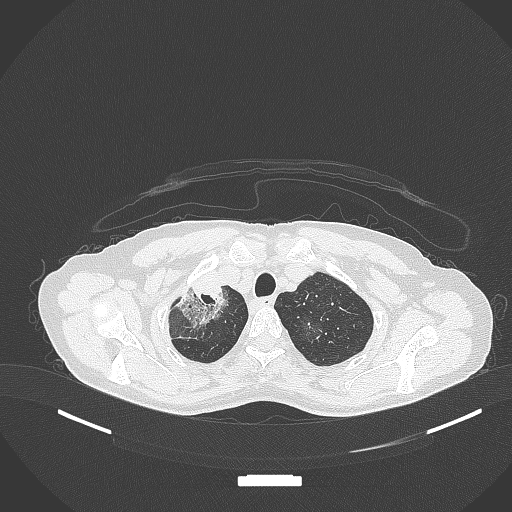
Chest CT, one axial slice. Position 283 of 284 along the scan axis. Reconstruction kernel B70f. 120 kVp. Lung window (W 1500 / L -600 HU). 1 mm slice thickness. 512 × 512 image matrix. Patient: female, 59 years. Case-level facts recorded for this patient, not image findings: clinical TNM (as recorded): T3 N0 M0; histopathological grade: G1.
Outlined on this slice (rectangle marked by the reading radiologist):
- lung tumour (recorded histology: adenocarcinoma): bounding box <172,278,224,330> (left, top, right, bottom; pixels)